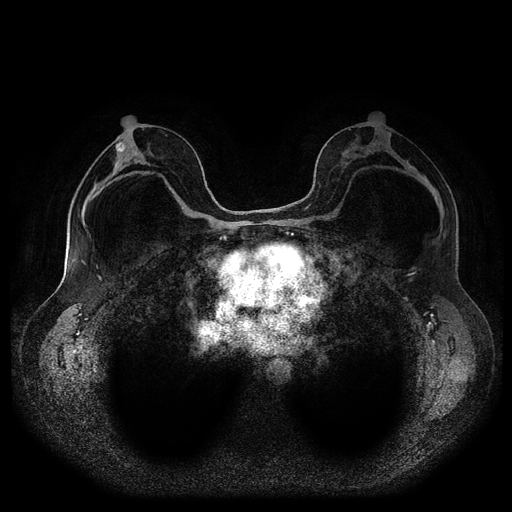
Breast MRI (dynamic contrast-enhanced, multi-phase), one axial slice; position 54 of 116 along the scan axis; dynamic contrast-enhanced series, time point 2 of 5 at this slice position (early post-contrast); 1.5 T; TE 2.6 ms, TR 5.3 ms; 512 × 512 image matrix, field of view 360 × 360 mm. Patient: female, 46 years.
Annotated regions visible in this slice (semi-automatically segmented with operator editing):
- breast lesion (labelled 'tumour' in the annotation; benign lesions carry a separate 'benign' label): bounding box (x1, y1, x2, y2) in pixels: (116, 142, 125, 152)